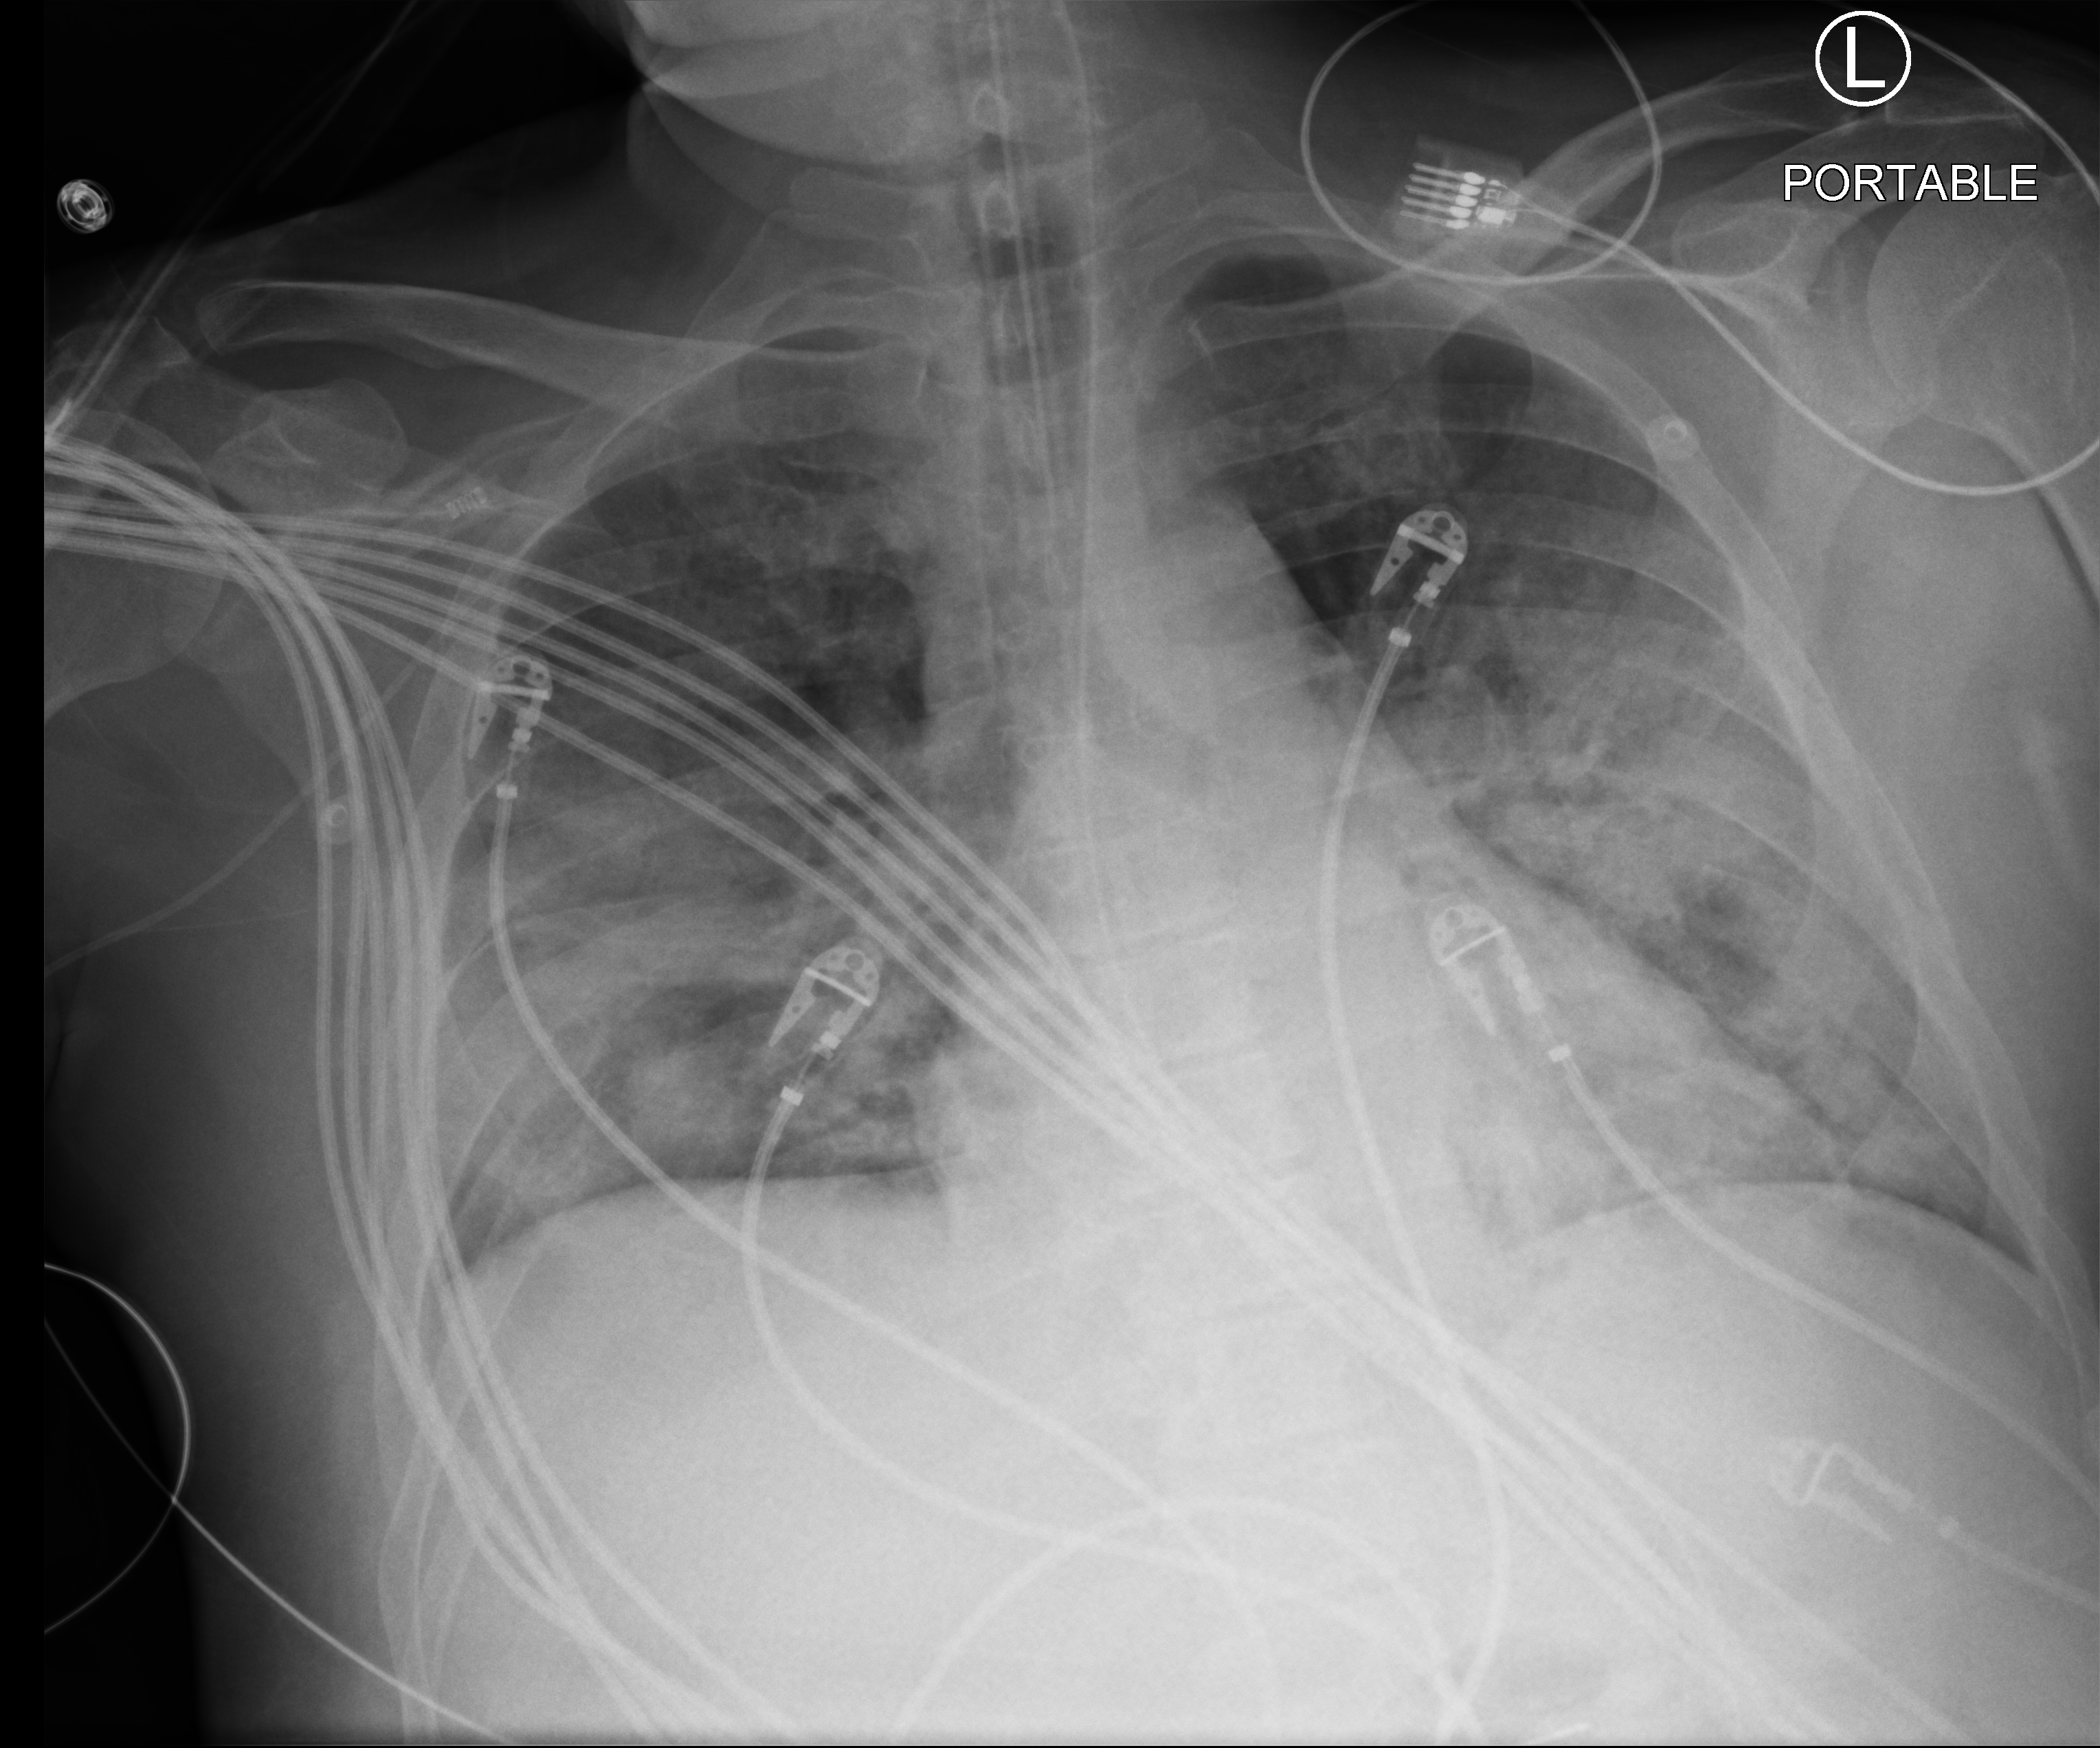
Chest X-ray (portable). Male patient hospitalised with COVID-19, age 18–59 years.
Admission-level facts for this patient (not findings on this image; timing relative to this image not recorded): mechanically ventilated during this hospital stay: yes.